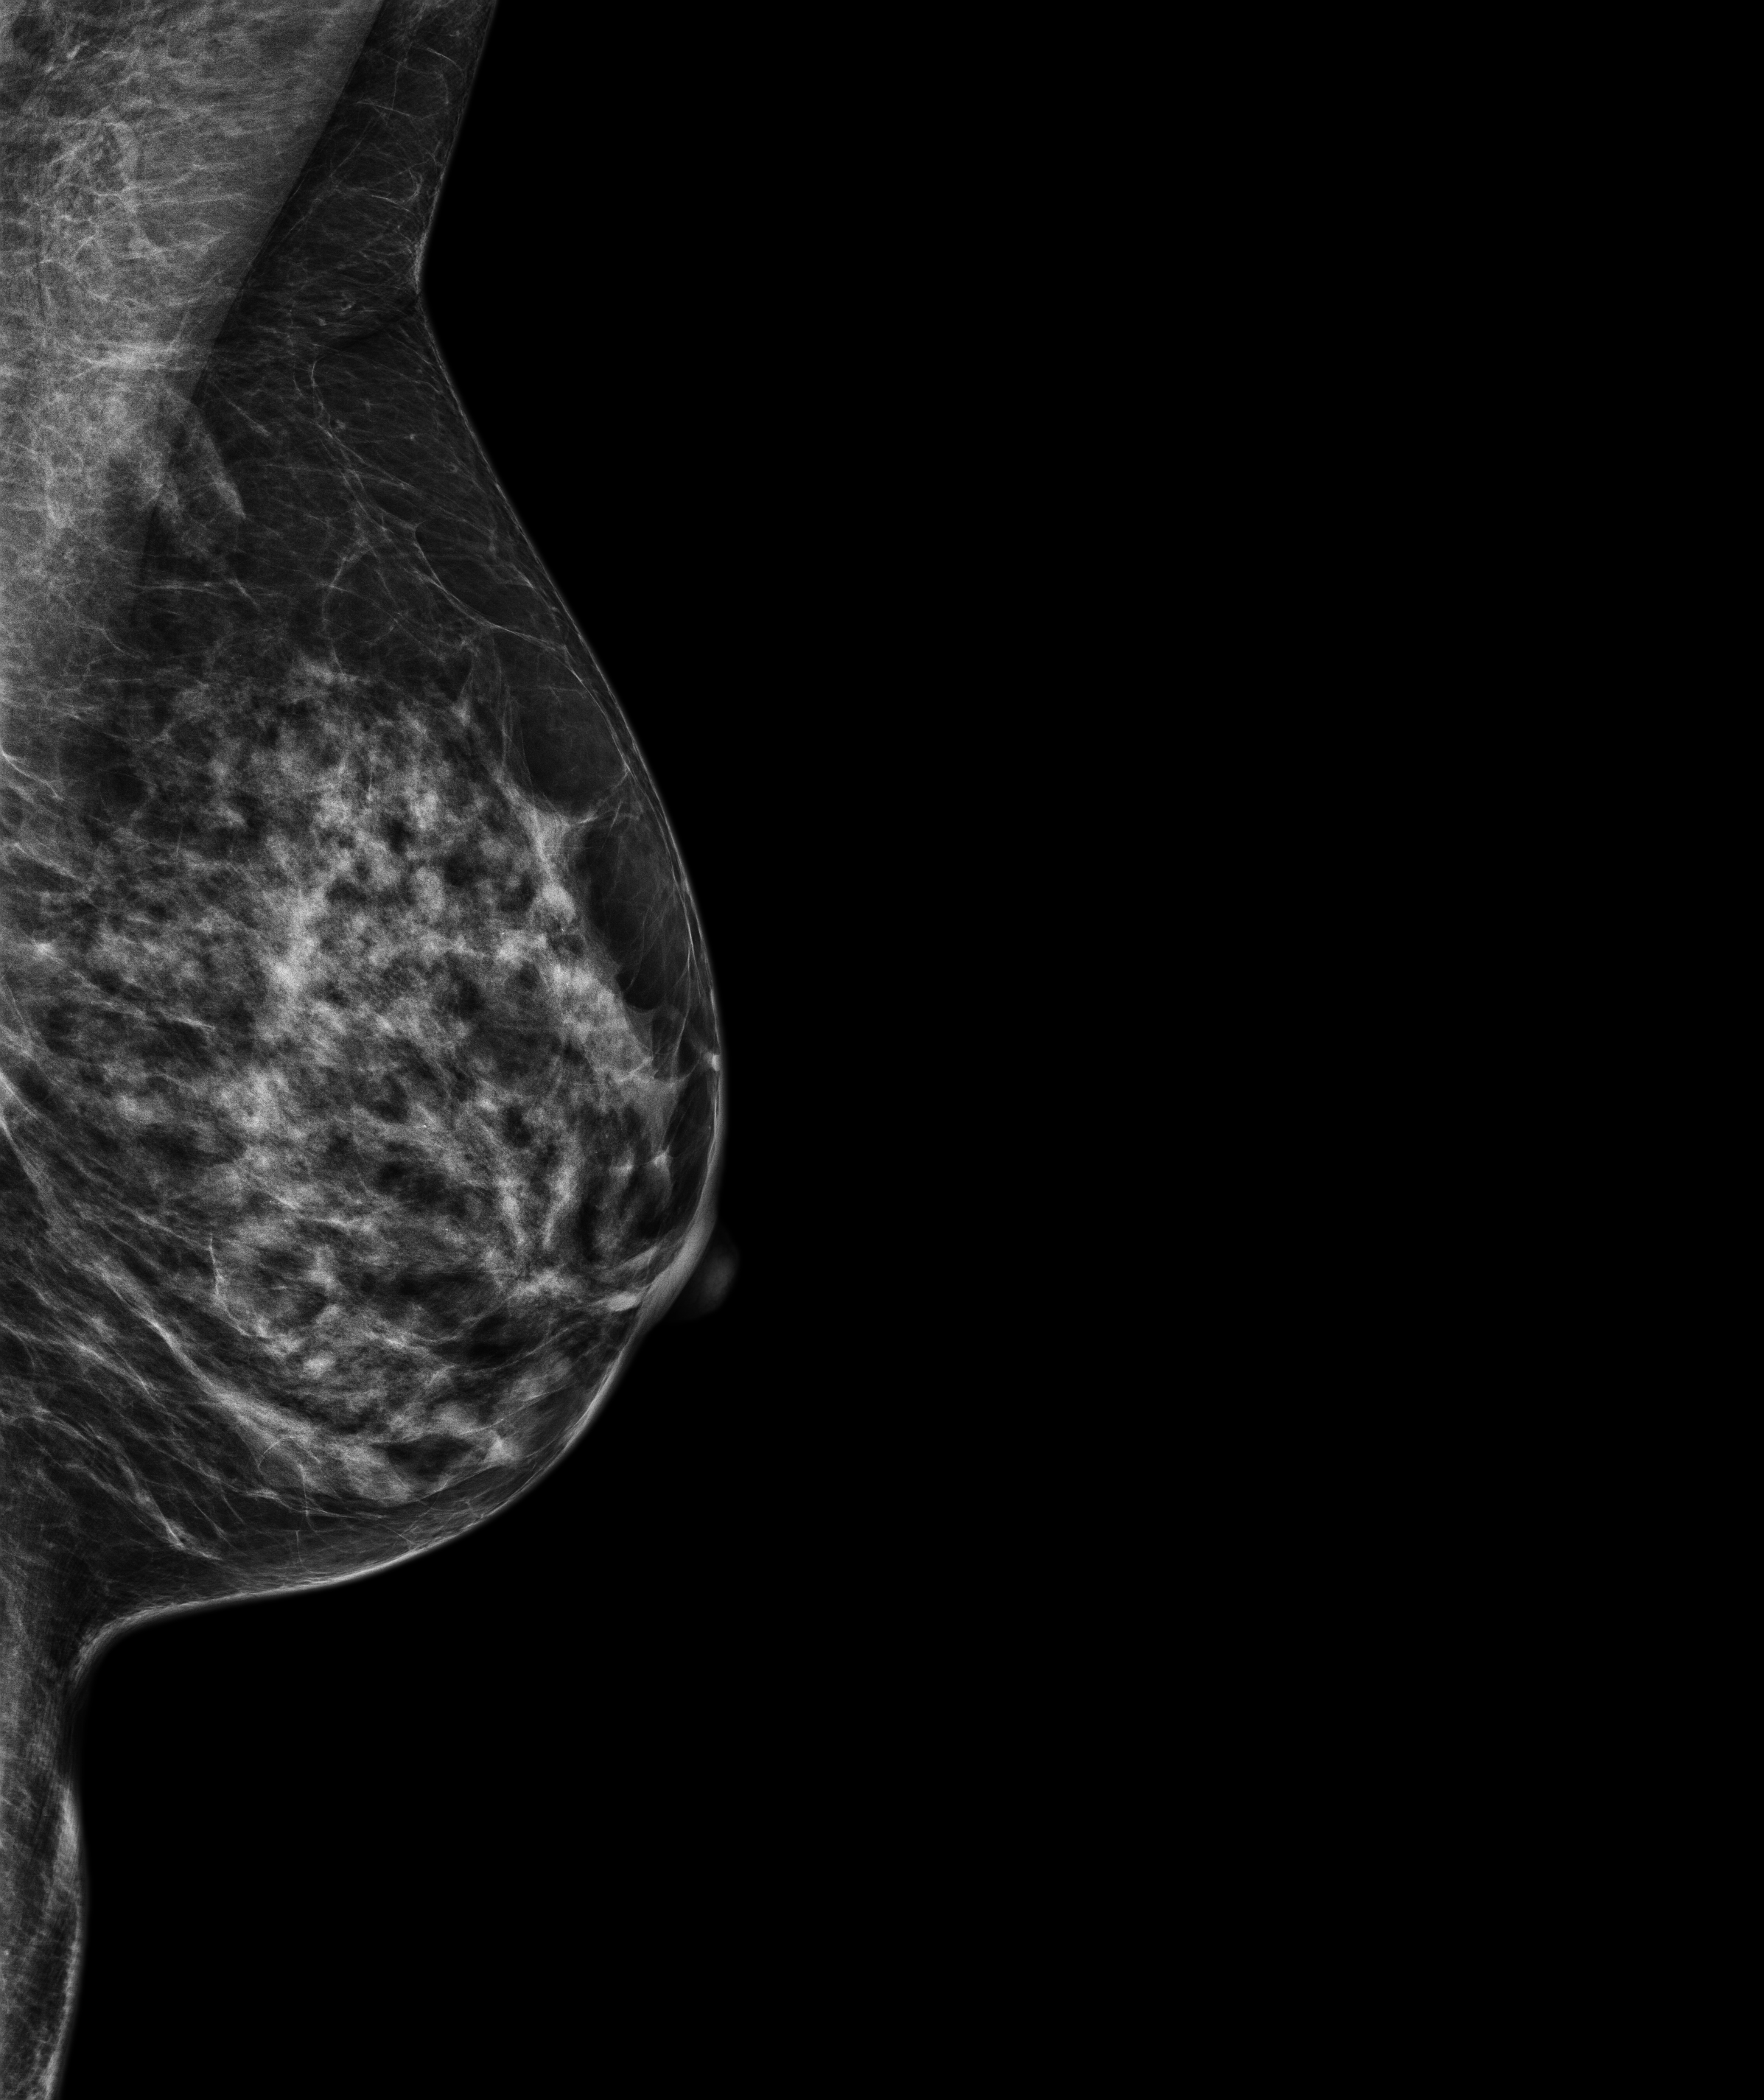
Screening examination; compressed breast thickness 50.2 mm; system: Senographe Pristina. Patient: female, 59 years.
Image type: full-field digital mammogram. Breast: left. Projection: mediolateral oblique (MLO) view.